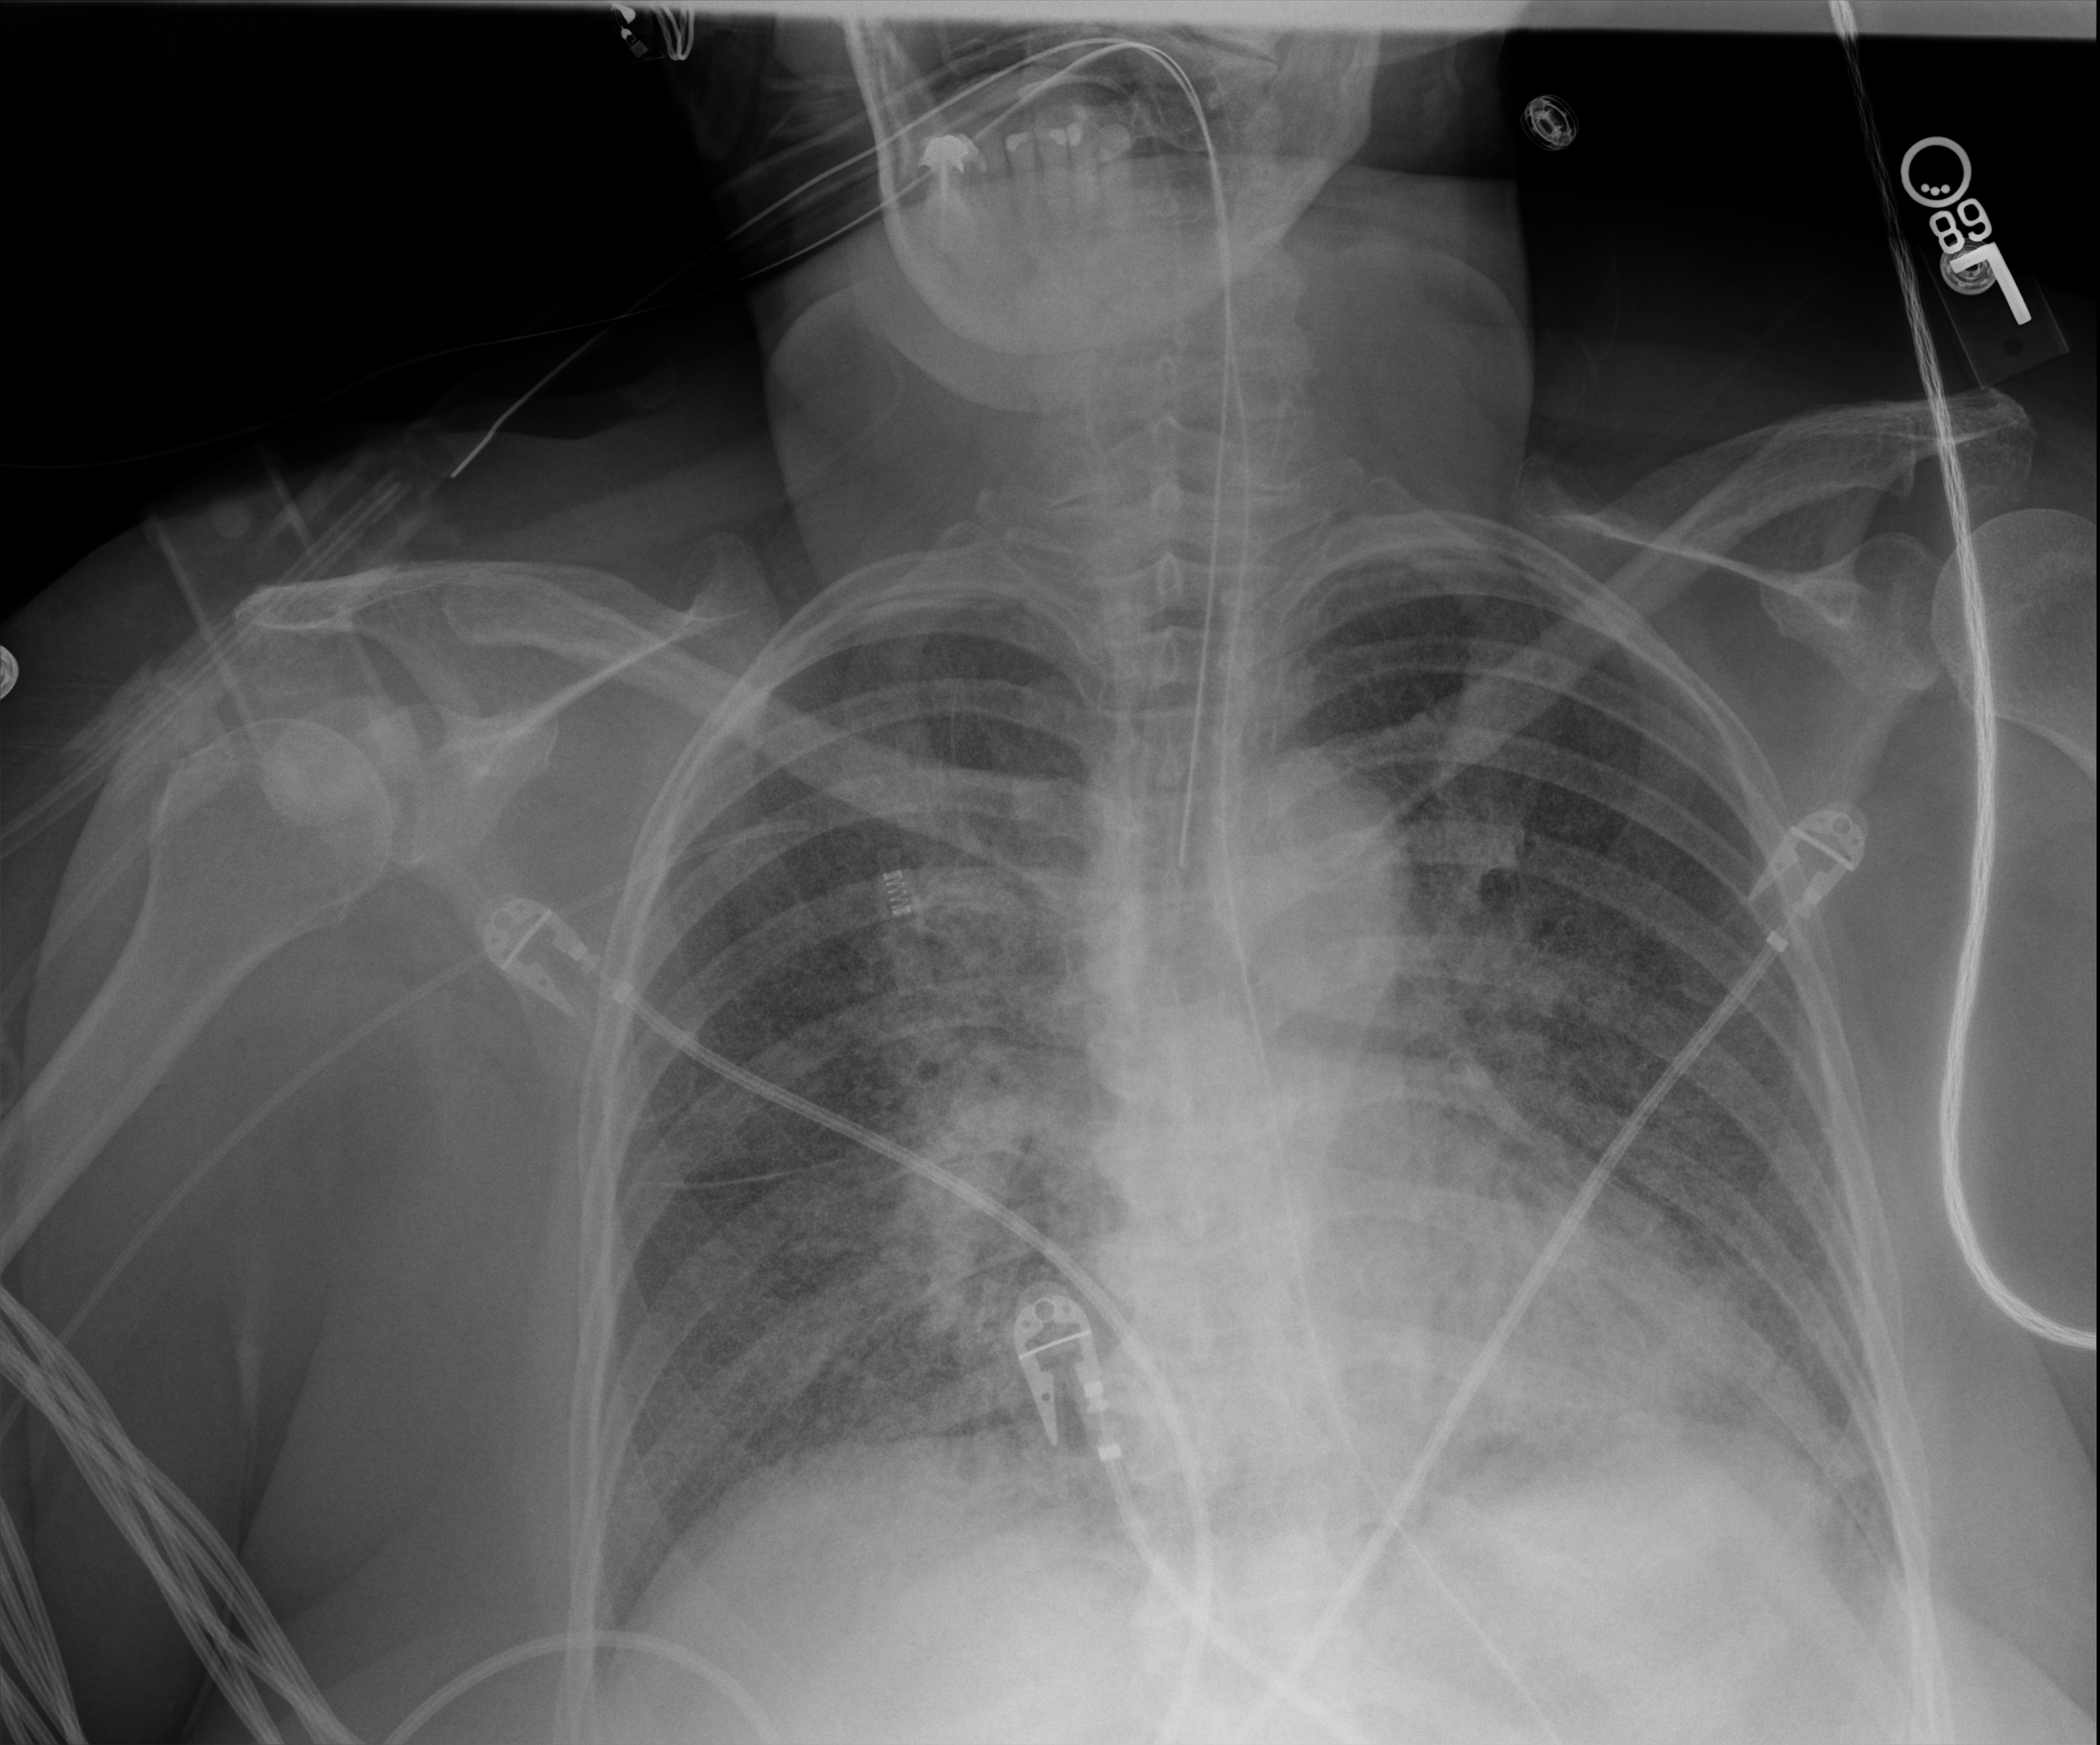
Chest X-ray, anteroposterior (AP) projection. Patient hospitalised with COVID-19; female, aged 60–74 years.
Admission-level facts for this patient (not findings on this image; timing relative to this image not recorded): mechanically ventilated during this hospital stay: yes; other chronic lung disease (admission record): no.